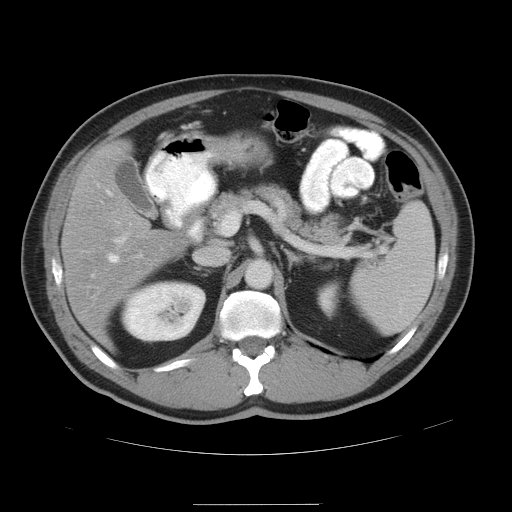
Contrast-enhanced abdominal CT, one axial slice; slice 26 of 47 in the series (ordered by position); 120 kVp; intravenous contrast given; soft-tissue window (W 400 / L 40 HU); 5 mm slice thickness; 512 × 512 image matrix, field of view 420 × 420 mm. Male patient, age 61 years. Case-level facts recorded for this patient, not image findings: diagnosis: colorectal cancer liver metastases, imaged before liver resection; multiple liver metastases: no; largest metastasis: 1.2 cm; disease in both lobes: no.
Annotated regions visible in this slice (manually delineated by an expert):
- hepatic veins: bounding box (x1, y1, x2, y2) in pixels: (108, 190, 119, 262)
- liver: (63, 144, 187, 343)
- planned liver remnant (the part of the liver to remain after resection): (68, 144, 187, 342)
- portal vein (with intrahepatic branches): (116, 237, 125, 241)